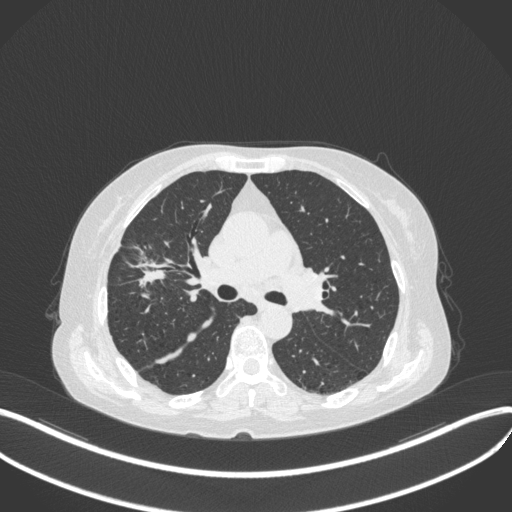
Chest CT, one axial slice. Slice 245 of 429 in the series (ordered by position). Reconstruction kernel B31f. 120 kVp. Lung window (W 1500 / L -600 HU). 512 × 512 image matrix, field of view 400 × 400 mm. Patient: female, 69 years. From the clinical record (not read from this slice): clinical TNM (as recorded): T1b N3 M0.
Structures marked on this image (bounding box drawn by a radiologist):
- lung tumour (recorded histology: small cell carcinoma): bounding box <115,244,173,289> (left, top, right, bottom; pixels)